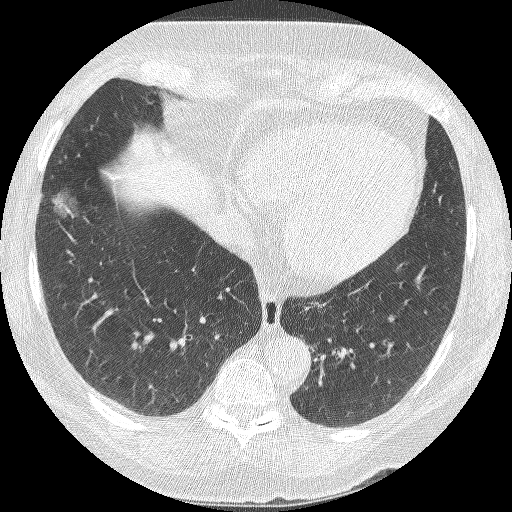
Low-dose screening chest CT, axial slice, second annual screen, lung window (W 1500 / L -600 HU), 1.25 mm slice thickness, lung (sharp) reconstruction kernel (BONE), 512 × 512 image matrix, field of view 310 × 310 mm. Female, age 68 years at enrolment. Current smoker at enrolment.
Expert-annotated lung lesion, box from (x=35, y=191) to (x=81, y=243) px. Reader record for this screening exam (exam-level; its link to the box is not recorded): non-calcified nodule or mass ≥4 mm, right lower lobe, 18 × 15 mm, poorly defined margins, ground glass attenuation, pre-existing on the prior screen: yes; interval growth: yes. Lung cancer was diagnosed 42 days after this screen: bronchiolo-alveolar adenocarcinoma, NOS, right lower lobe, well differentiated (G1), stage IA (AJCC 6th edition), 13 mm at pathology.